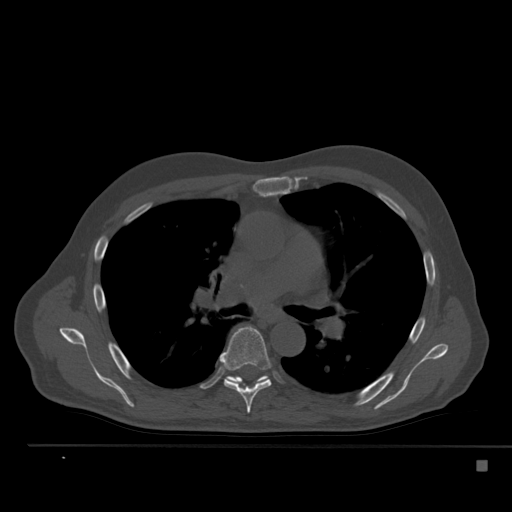
CT including the spine, one axial slice; position 343 of 517 along the scan axis; 120 kVp; bone window (W 1800 / L 400 HU); 1.5 mm slice thickness; 512 × 512 image matrix, field of view 408 × 408 mm. Patient: male, 70 years. Case-level facts recorded for this patient, not image findings: primary cancer: renal.
Structures marked on this image (semi-automatic segmentation, software-assisted and operator-edited):
- T6 vertebra: bounding box (x1, y1, x2, y2) in pixels: (219, 326, 271, 414)
- T7 vertebra: (225, 375, 270, 383)